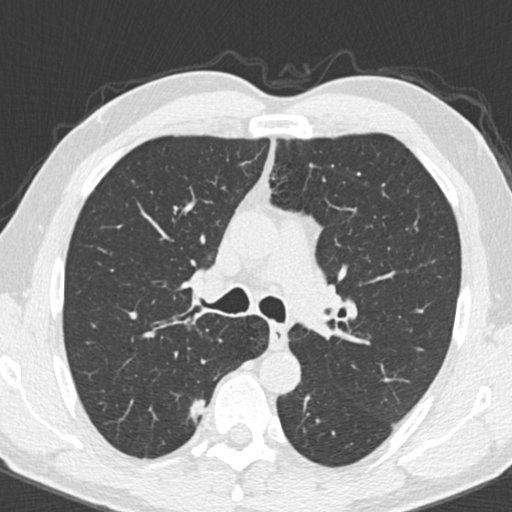
Low-dose screening chest CT, axial slice, third annual screen, lung window (W 1500 / L -600 HU), 512 × 512 image matrix, field of view 307 × 307 mm. Male participant, aged 55 years at enrolment. Current smoker at enrolment.
Expert-annotated lung lesion, bounding box <170,391,219,438> (left, top, right, bottom; pixels). The exam's reader record, not a measurement of the box and not confirmed to be the same lesion: non-calcified nodule or mass ≥4 mm, right upper lobe, 9 × 7 mm, smooth margins, soft tissue attenuation, pre-existing on the prior screen: no. Lung cancer was diagnosed 221 days after this screen: adenocarcinoma, NOS, right upper lobe, poorly differentiated (G3), stage IA (AJCC 6th edition), 15 mm at pathology.